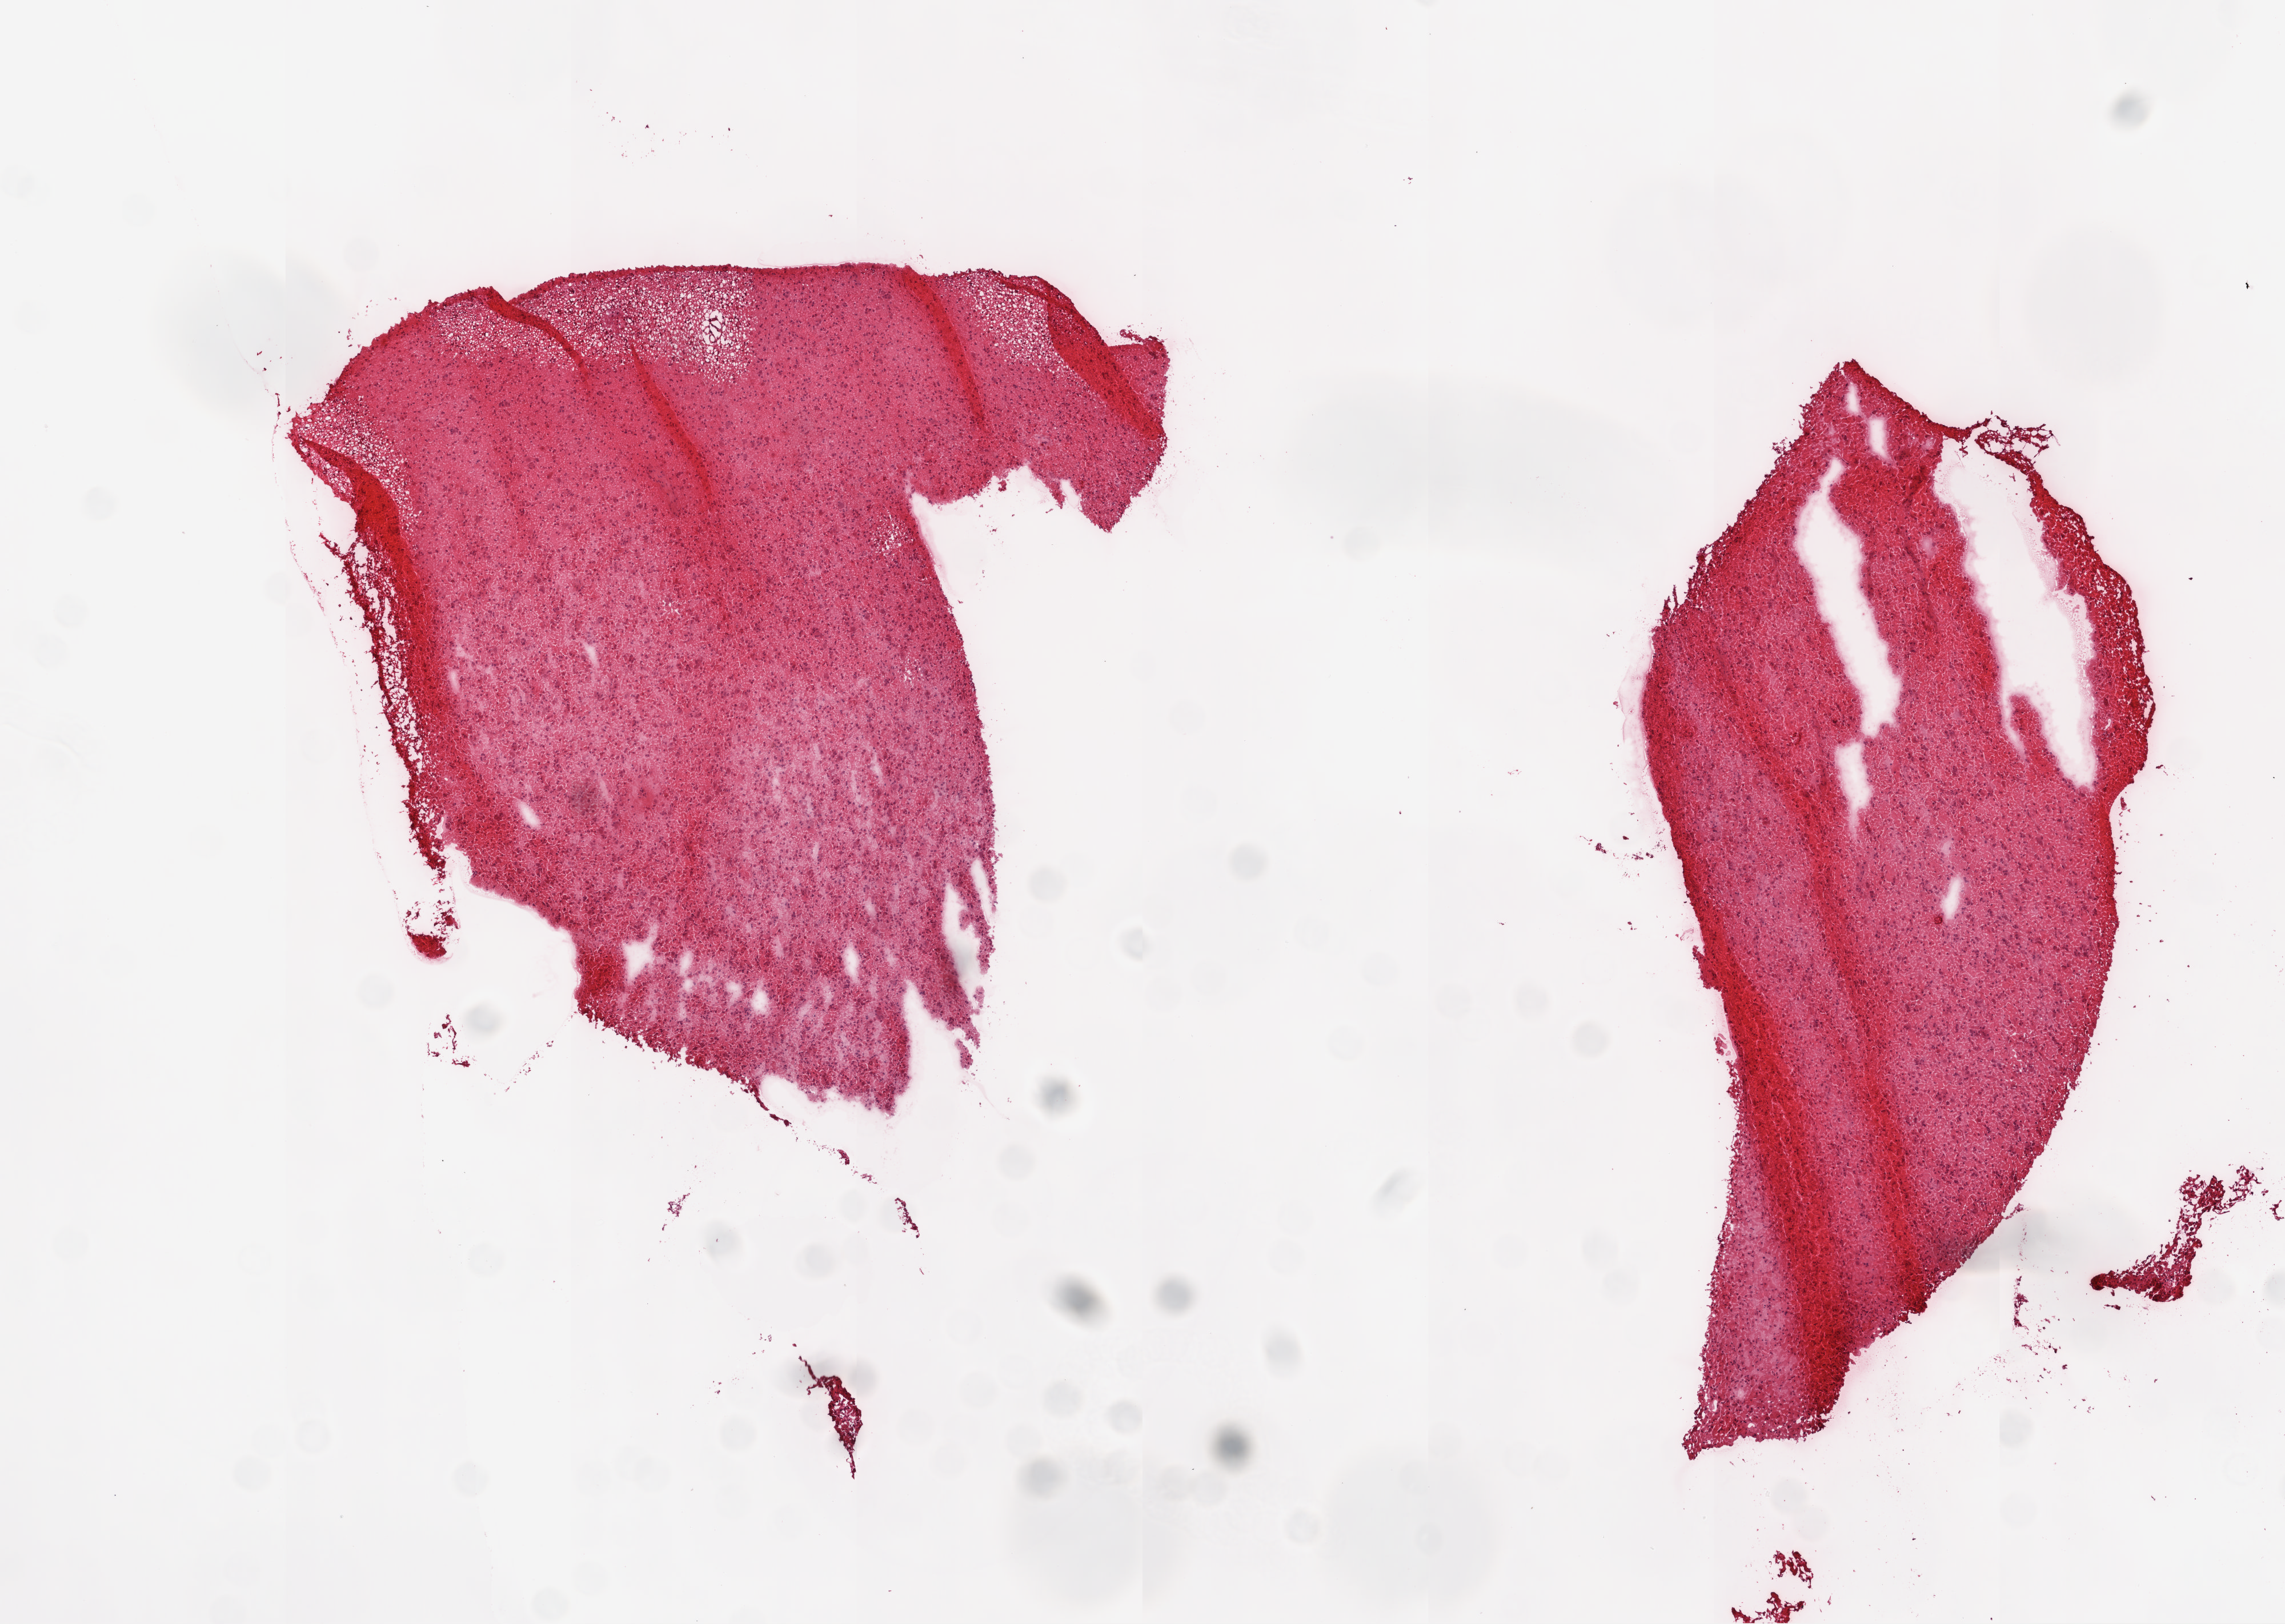
Digitized H&E-stained tissue section (whole slide), whole scanned area (about 8.0 x 5.7 mm, from a 20x scan) shown as a low-resolution overview; frozen section from the top of the tissue portion; primary tumour sample from the brain. Patient: female, age at initial diagnosis 48 years. Histologic grade: G2 (moderately differentiated). Pathologist review of this section (percent, as recorded): tumour nuclei 70%, normal cells 0%, stromal cells 0%, necrosis 0%.
* diagnosis: Oligodendroglioma, NOS